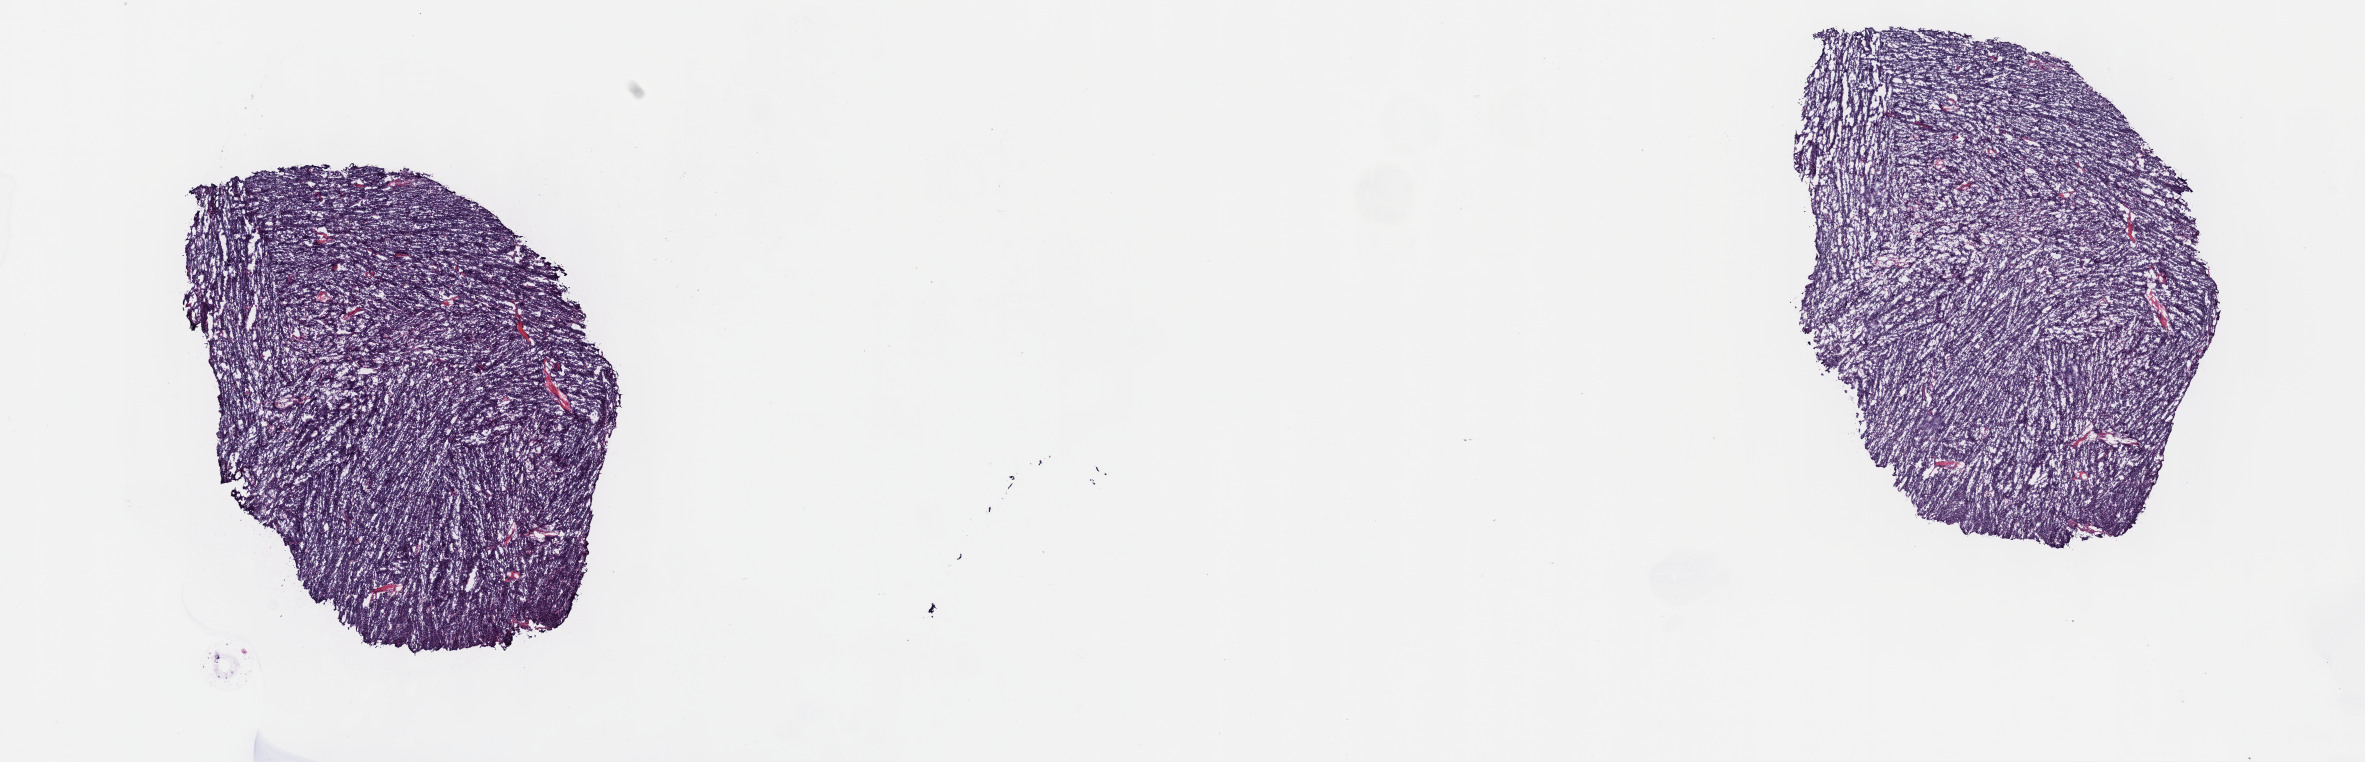
Whole-slide histology image, H&E-stained — a low-resolution overview of the entire scanned area, about 19.1 x 6.2 mm, frozen section from the top of the tissue portion, primary tumour sample from the thymus. Female, age 77 years at initial diagnosis. Pathologist review of this section (percent, as recorded): tumour cells 100%, tumour nuclei 97%, normal cells 0%, stromal cells 0%, necrosis 0%. Infiltration values recorded for this section: lymphocyte infiltration 0%, monocyte infiltration 0%, neutrophil infiltration 0%.
* diagnosis: Thymoma, type AB, malignant